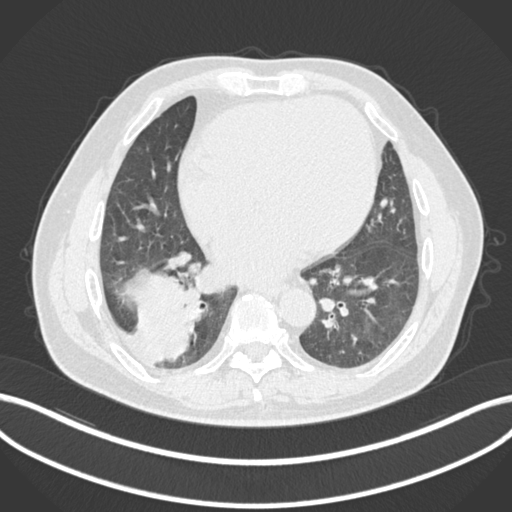
Chest CT, one axial slice. Position 59 of 200 along the scan axis. Reconstruction kernel B30f. 120 kVp. Lung window (W 1500 / L -600 HU). 1 mm slice thickness. 512 × 512 image matrix, field of view 400 × 400 mm. Patient: male, 59 years.
Structures marked on this image (rectangle marked by the reading radiologist):
- lung tumour (recorded histology: adenocarcinoma): bounding box <128,266,196,362> (left, top, right, bottom; pixels)